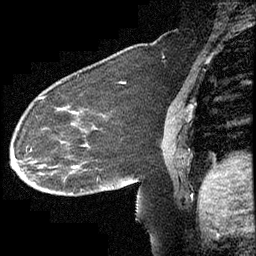
Breast MRI (dynamic contrast-enhanced), one sagittal slice; position 154 of 232 along the scan axis; dynamic contrast-enhanced study with each time point stored as its own series, time point 2 of 4 at this slice position (early post-contrast, ordered by acquisition time); 1.5 T; TE 4.2 ms, TR 6.7 ms; 3 mm slice thickness; 256 × 256 image matrix. Patient: female, 63 years. Case-level facts recorded for this patient, not image findings: setting: breast cancer imaged before/during neoadjuvant chemotherapy; receptor status: triple-negative.
Outlined on this slice (semi-automatically segmented with operator editing):
- analysis volume of interest (the breast-tissue region the enhancement analysis was run in; not a lesion): bounding box [x1, y1, x2, y2] px = [13, 90, 140, 211]
- tumour enhancement mask (voxels above the 70 % enhancement threshold inside the analysis volume of interest): [41, 96, 78, 167]